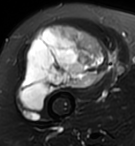
MRI of an extremity soft-tissue mass, one axial slice; position 65 of 95 along the scan axis; T2-weighted fat-saturated; MR volume resampled by the dataset authors to the PET/CT grid (not the native acquisition matrix); 3.27 mm slice thickness; 135 × 146 image matrix. Female patient. Case-level facts recorded for this patient, not image findings: histological type: pleiomorphic undifferentiated sarcoma; grade: high; site of the primary tumour: right quadricep.
Outlined on this slice (expert contour drawn on MRI and transferred to this co-registered scan by the dataset authors):
- gross tumour volume including surrounding oedema: bounding box (x1, y1, x2, y2) in pixels: (19, 25, 109, 112)
- gross tumour volume (mass): (19, 25, 109, 112)